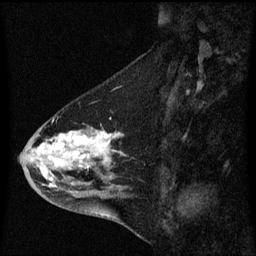
Breast MRI (dynamic contrast-enhanced), one sagittal slice. Slice 25 of 60 in the series (ordered by position). Dynamic contrast-enhanced series, image 2 of 3 at this slice position (ordered by acquisition). 1.5 T. TE 4.2 ms, TR 8.4 ms. 2 mm slice thickness. 256 × 256 image matrix, field of view 200 × 200 mm. Patient: female, 46 years. Case-level facts recorded for this patient, not image findings: setting: breast cancer imaged before/during neoadjuvant chemotherapy; receptor status: HER2-positive.
Structures marked on this image (semi-automatically segmented with operator editing):
- analysis volume of interest (the breast-tissue region the enhancement analysis was run in; not a lesion): bounding box (x1, y1, x2, y2) in pixels: (19, 116, 131, 195)
- tumour enhancement mask (voxels above the 70 % enhancement threshold inside the analysis volume of interest): (43, 132, 122, 187)